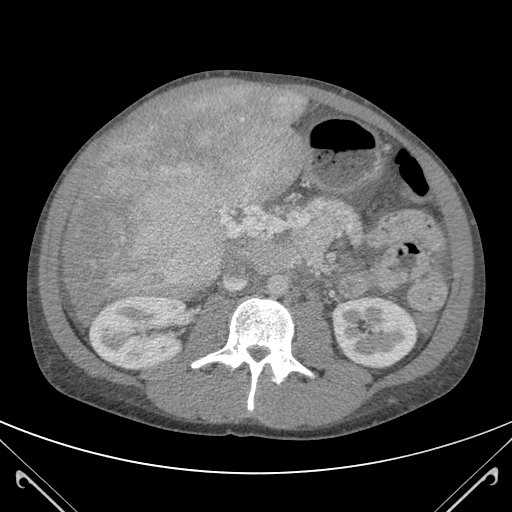
Contrast-enhanced abdominal CT (liver protocol), one axial slice. 120 kVp. Soft-tissue window (W 400 / L 40 HU). 3 mm slice thickness. 512 × 512 image matrix. From the clinical record (not read from this slice): diagnosis: hepatocellular carcinoma (patient treated with transarterial chemoembolisation; whether this scan precedes or follows treatment is not stated here); TNM stage (as recorded): Stage-IIIB; Child-Pugh class: A; tumour nodularity: uninodular.
Annotated regions visible in this slice (semi-automatically segmented with operator editing):
- abdominal aorta: bounding box (x1, y1, x2, y2) in pixels: (267, 276, 287, 296)
- liver parenchyma outside the tumour (the mass and vessels are separate outlines, so this box may not span the whole liver): (59, 84, 311, 320)
- mass: (88, 86, 306, 300)
- liver vessels: (113, 217, 224, 299)